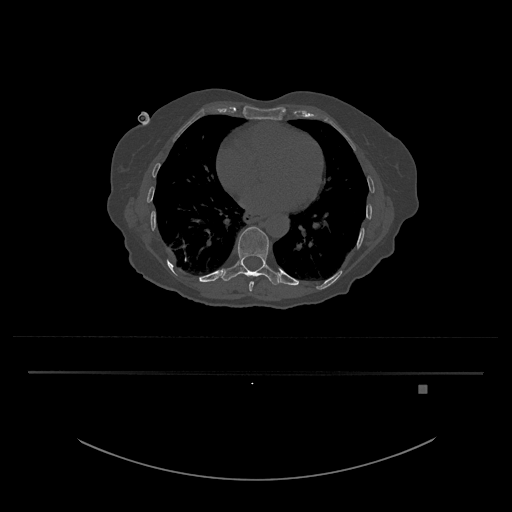
CT including the spine, one axial slice. Position 724 of 797 along the scan axis. 120 kVp. Bone window (W 1800 / L 400 HU). 0.5 mm slice thickness. 512 × 512 image matrix, field of view 500 × 500 mm. Patient: female, 57 years. Case-level facts recorded for this patient, not image findings: primary cancer: cervical.
Annotated regions visible in this slice (semi-automatic segmentation, software-assisted and operator-edited):
- T10 vertebra: box from (x=221, y=226) to (x=284, y=285) px
- T9 vertebra: (x=249, y=281)–(x=254, y=292)